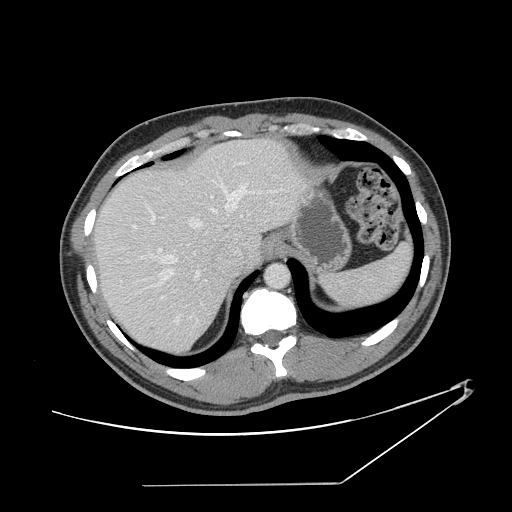
Contrast-enhanced abdominal CT, one axial slice. Position 115 of 152 along the scan axis. Reconstruction kernel STANDARD. 120 kVp. Intravenous contrast given. Soft-tissue window (W 400 / L 40 HU). 2.5 mm slice thickness. 512 × 512 image matrix, field of view 432 × 432 mm. Male patient, age 45 years. Case-level facts recorded for this patient, not image findings: diagnosis: colorectal cancer liver metastases, imaged before liver resection.
Annotated regions visible in this slice (expert manual segmentation):
- hepatic veins: box from (x=111, y=178) to (x=278, y=286) px
- liver: (x=96, y=139)–(x=304, y=353)
- planned liver remnant (the part of the liver to remain after resection): (x=96, y=162)–(x=233, y=353)
- portal vein (with intrahepatic branches): (x=158, y=248)–(x=207, y=323)